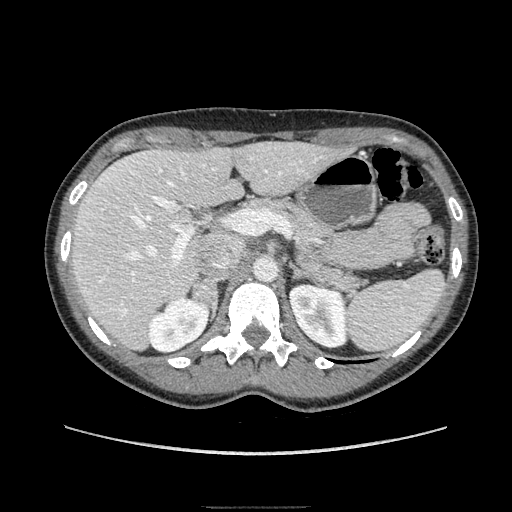
Contrast-enhanced abdominal CT, one axial slice. Slice 112 of 193 in the series (ordered by position). Soft-tissue window (W 400 / L 40 HU). 512 × 512 image matrix. Female patient. Case-level facts recorded for this patient, not image findings: diagnosis: adrenocortical carcinoma; tumour side: right adrenal; tumour size at pathology: 3 cm; Ki-67 index: 4 %; stage (as recorded): 1.
Outlined on this slice (semi-automatic segmentation, software-assisted and operator-edited):
- mass: bounding box <192,279,216,320> (left, top, right, bottom; pixels)